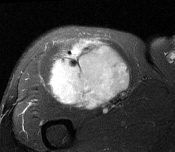
MRI of an extremity soft-tissue mass, one axial slice; T2-weighted fat-saturated; MR volume resampled by the dataset authors to the PET/CT grid (not the native acquisition matrix); 3.27 mm slice thickness; 175 × 152 image matrix, field of view 171 × 148 mm. Male patient. Case-level facts recorded for this patient, not image findings: histological type: pleiomorphic leiomyosarcoma; grade: intermediate; site of the primary tumour: right thigh.
Structures marked on this image (expert contour drawn on MRI and transferred to this co-registered scan by the dataset authors):
- gross tumour volume including surrounding oedema: bounding box [x1, y1, x2, y2] px = [49, 40, 130, 109]
- gross tumour volume (mass): [51, 40, 130, 109]